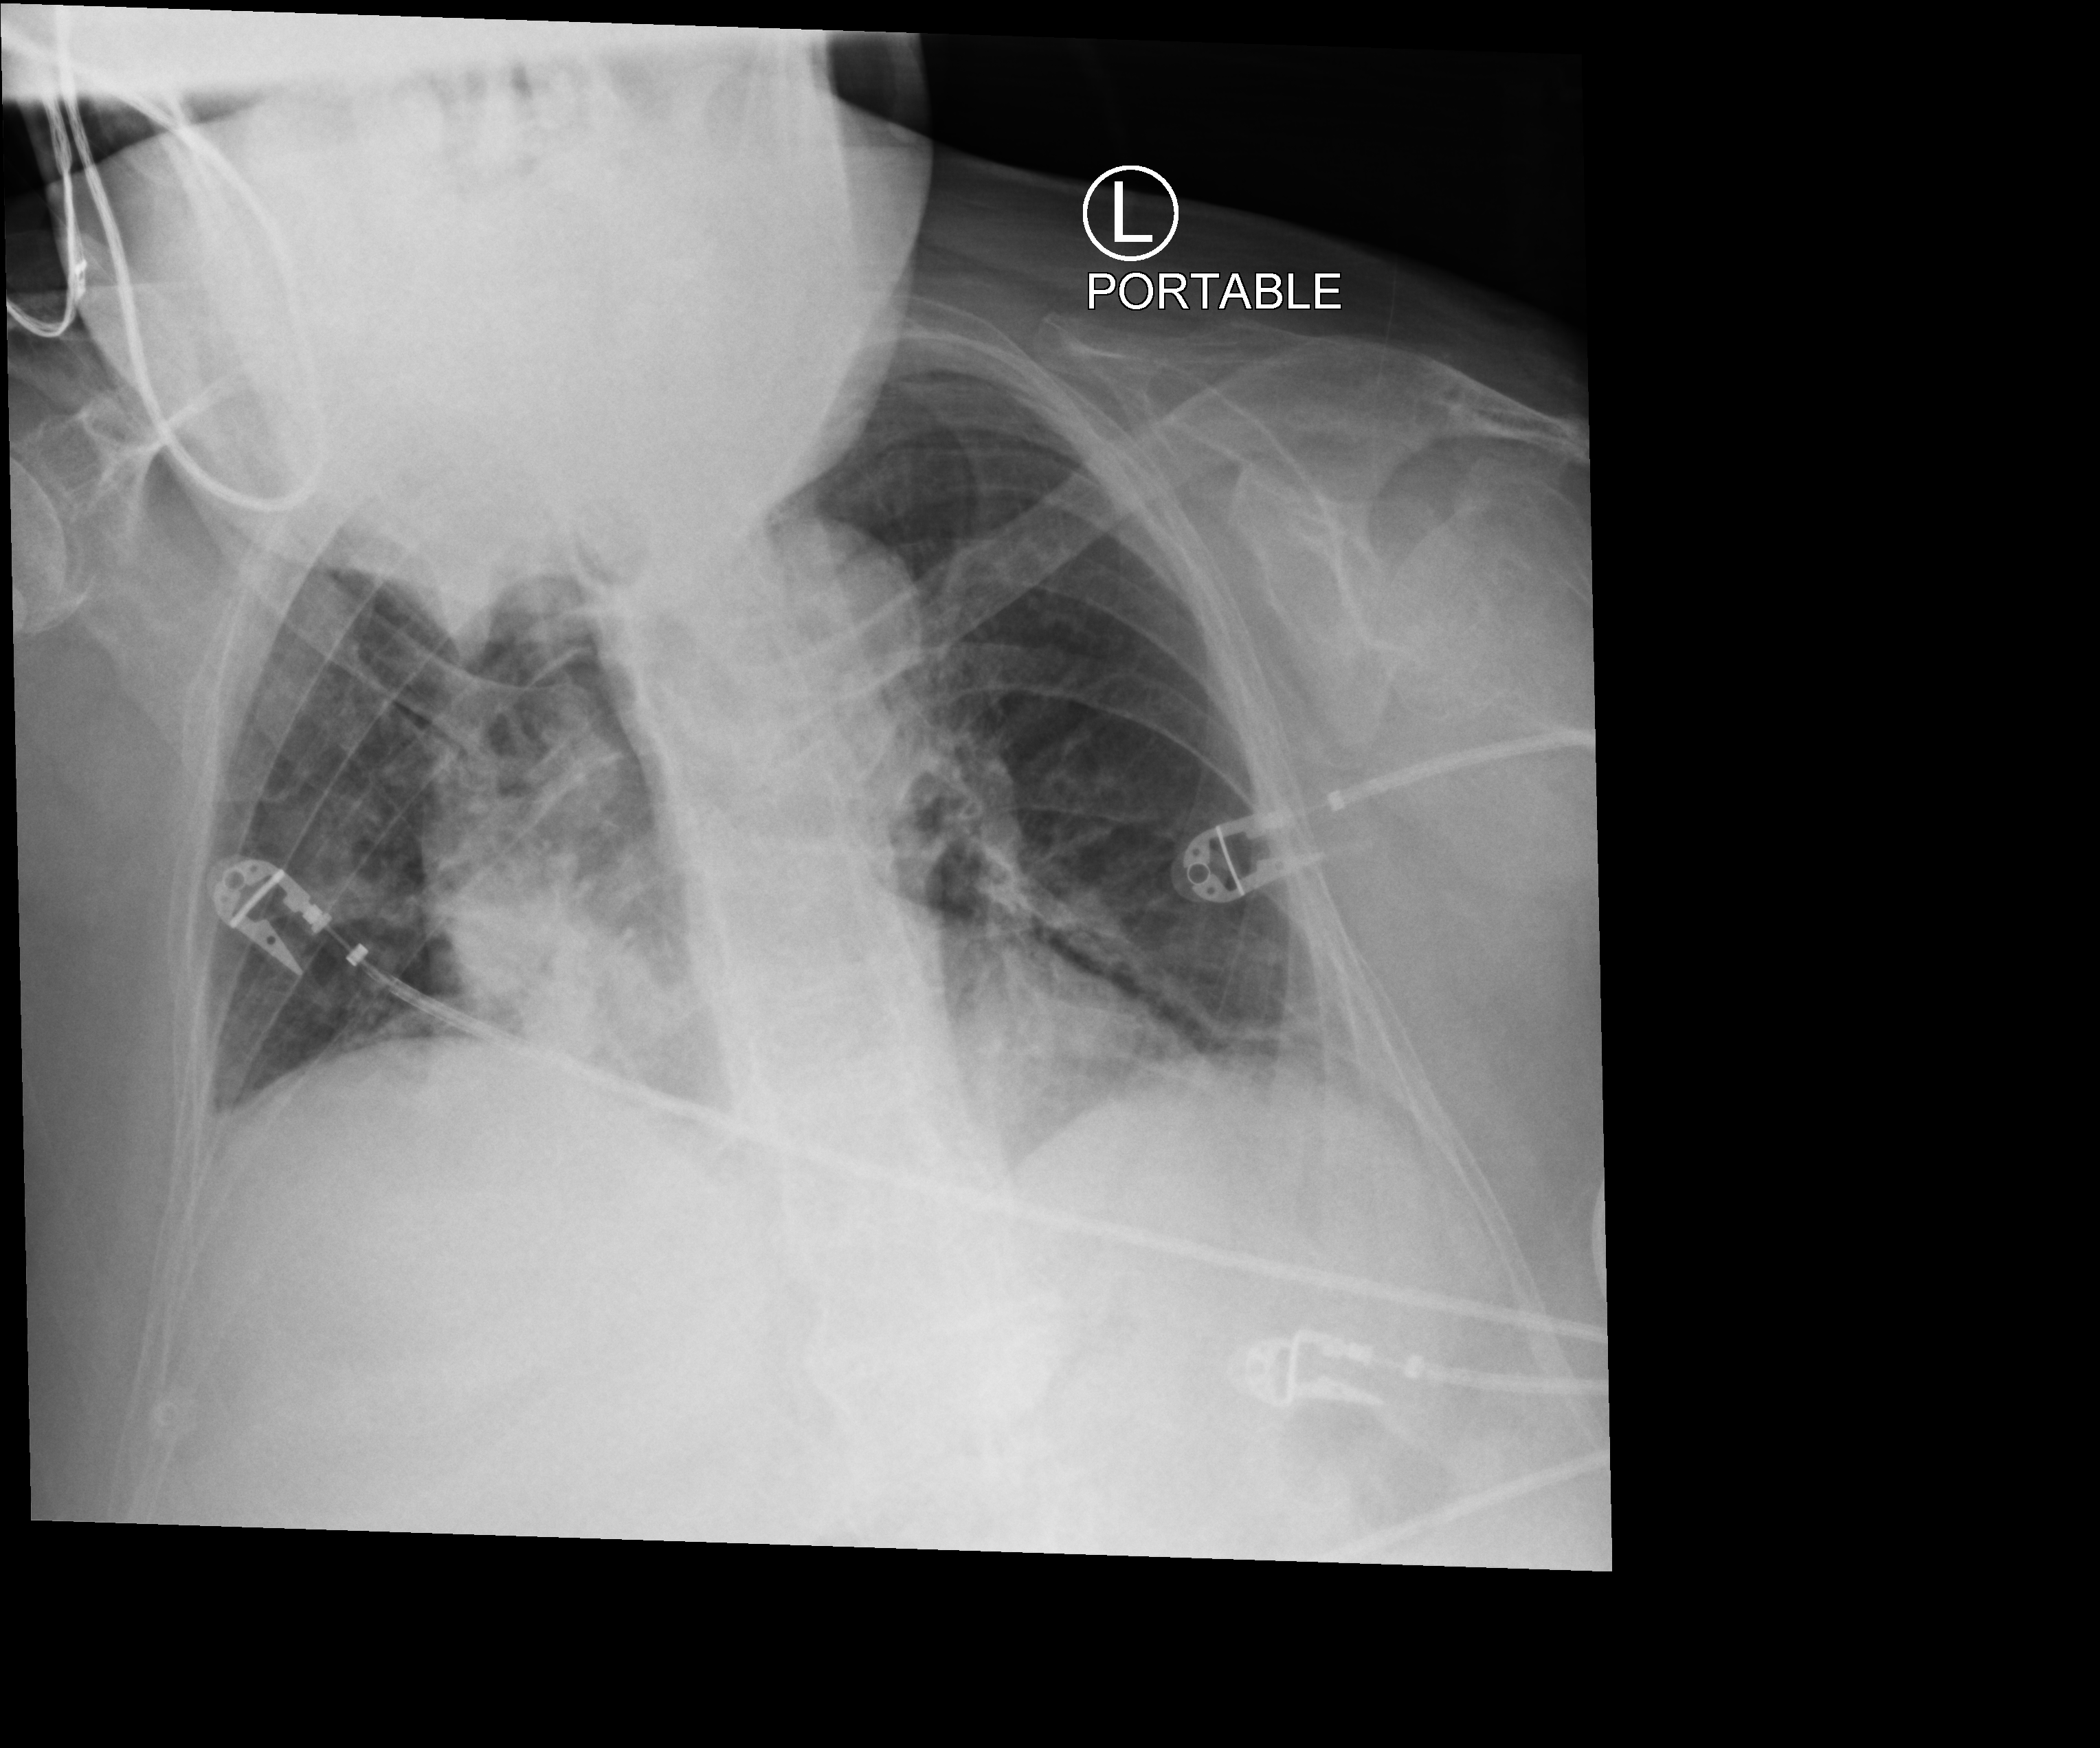
Bedside chest radiograph (computed radiography); anteroposterior (AP) projection. Patient hospitalised with COVID-19; female, aged 75–90 years.
Admission-level facts for this patient (not findings on this image; timing relative to this image not recorded): admitted to intensive care during this hospital stay: yes.